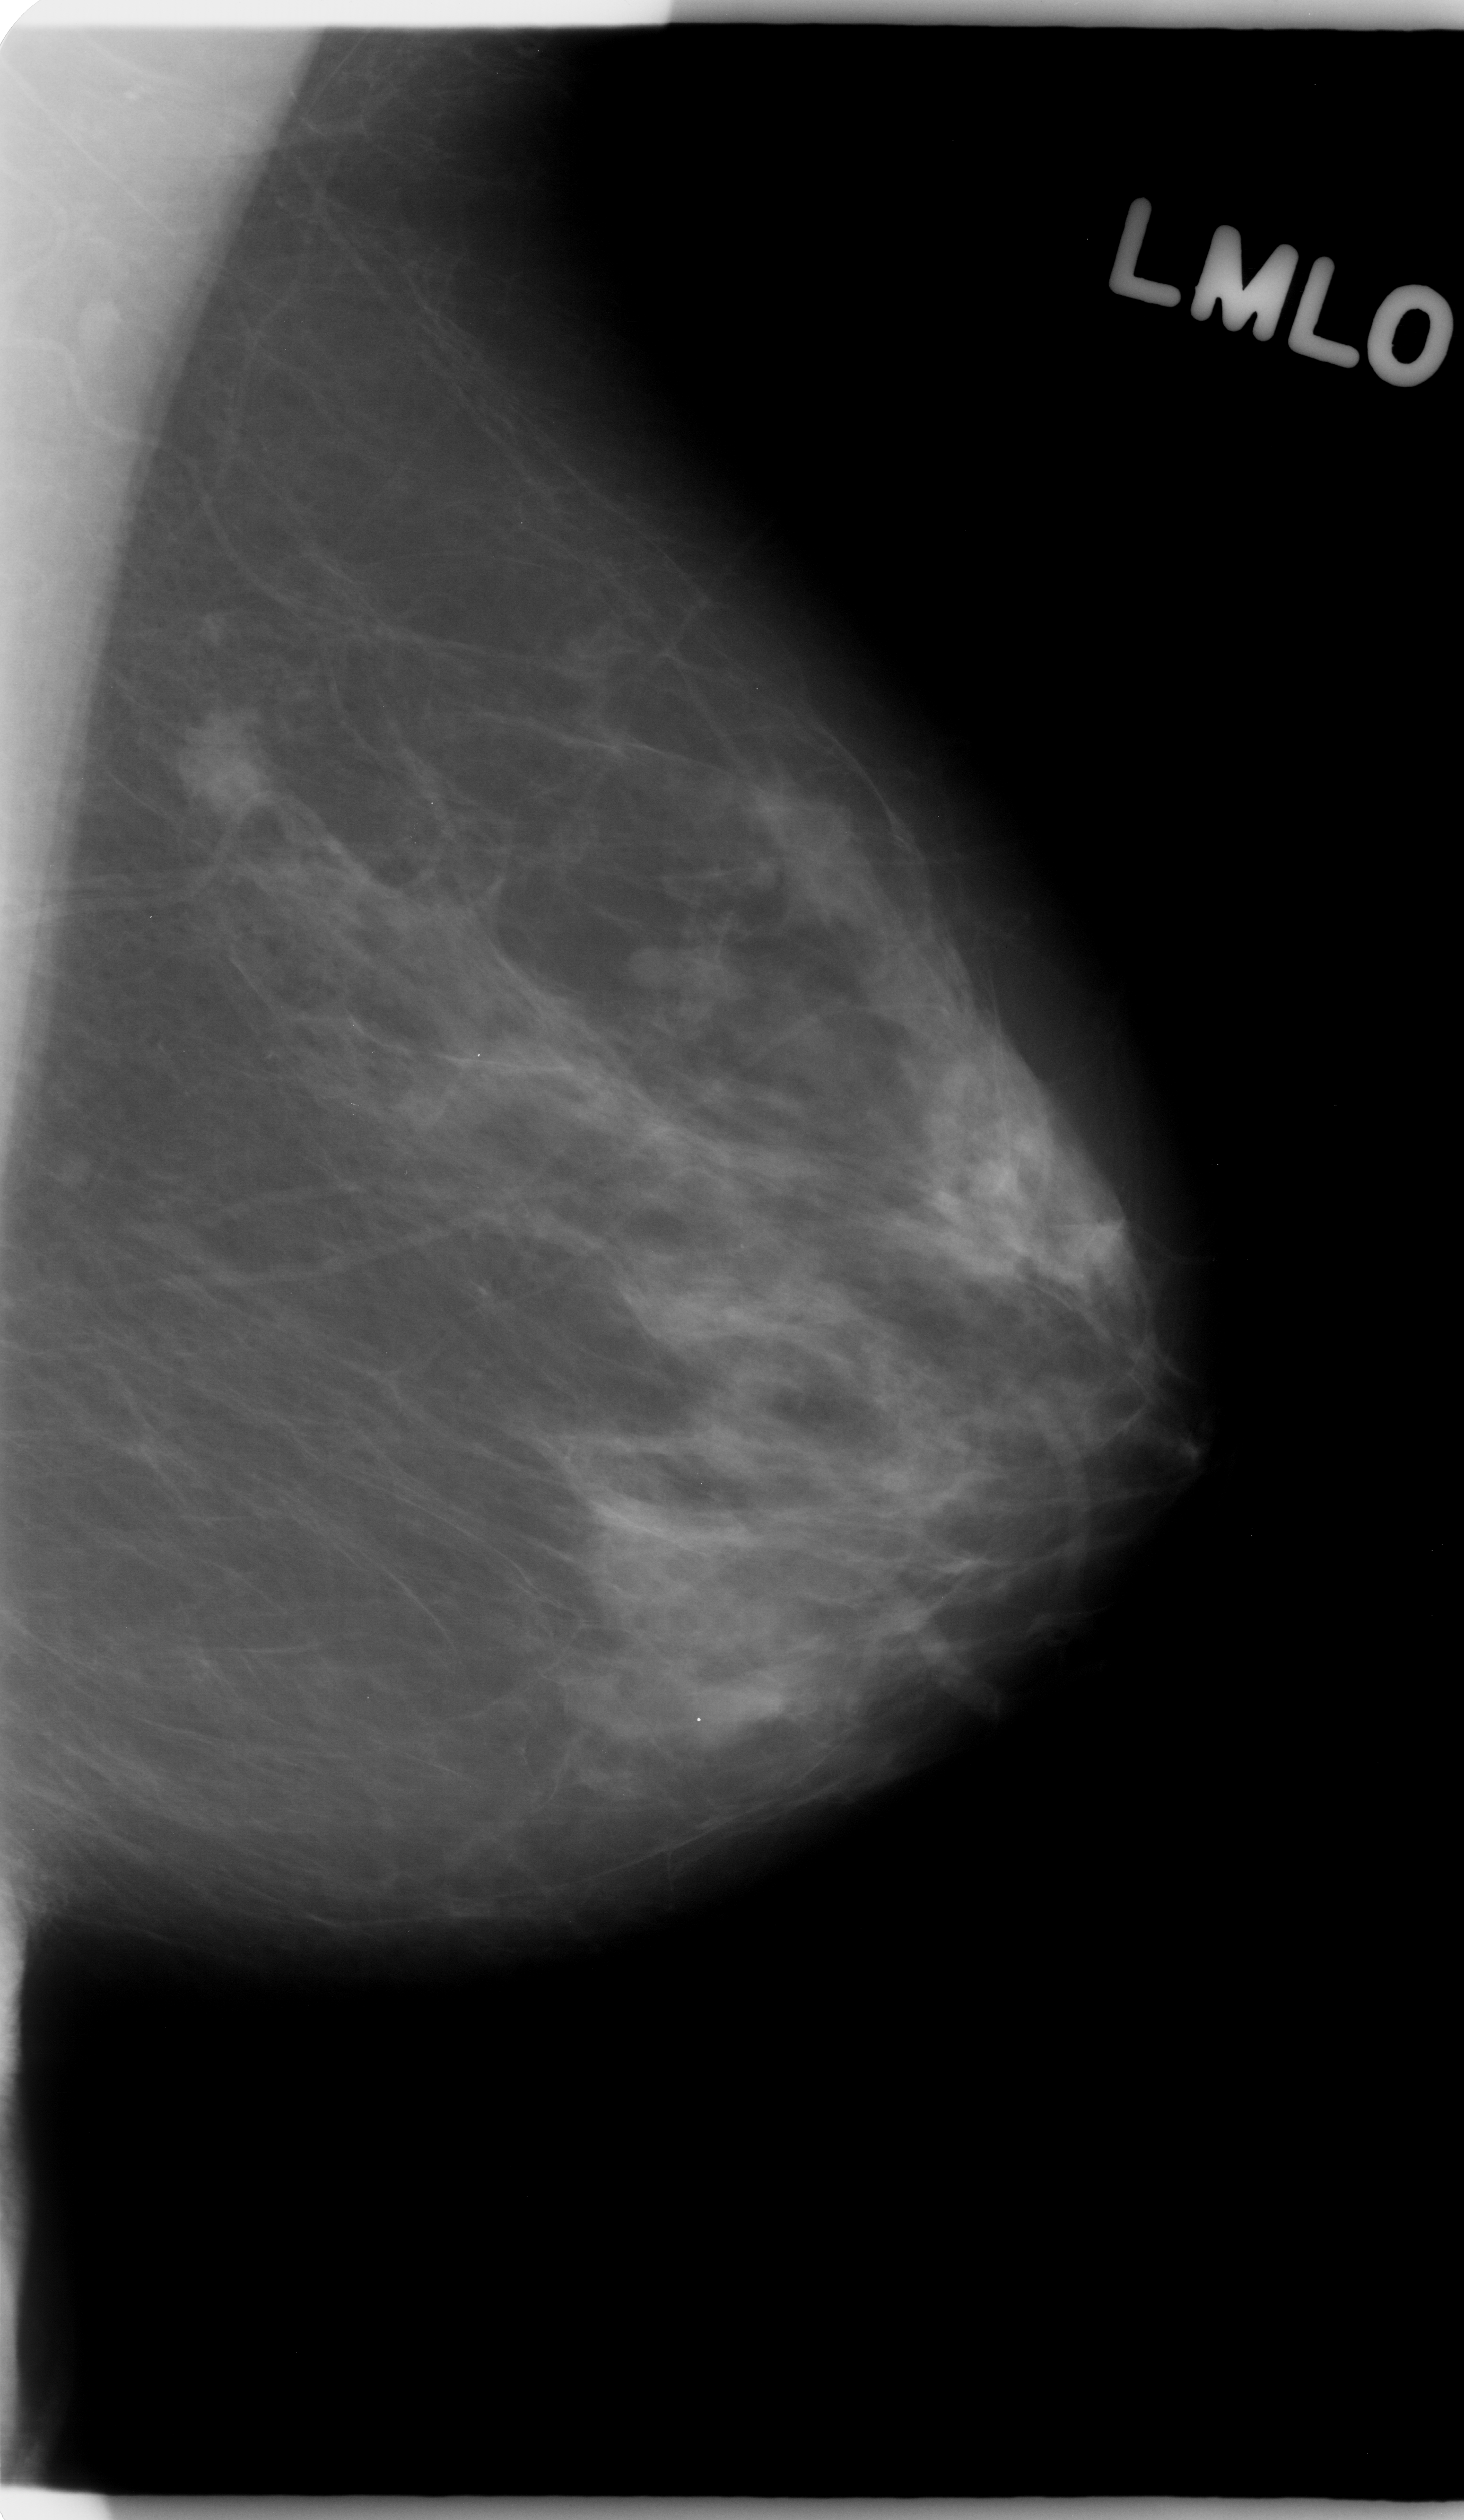
Scanned film-screen mammogram; left breast; mediolateral oblique (MLO) view; breast composition: scattered fibroglandular densities (BI-RADS density category 2 of 4); 1464 × 2520 image matrix.
Marked abnormalities (boxes around the expert regions of interest):
- mass, shape irregular, margins microlobulated; BI-RADS assessment category 4; pathology result (as recorded, not read from the image): malignant: bounding box [x1, y1, x2, y2] px = [163, 688, 291, 830]